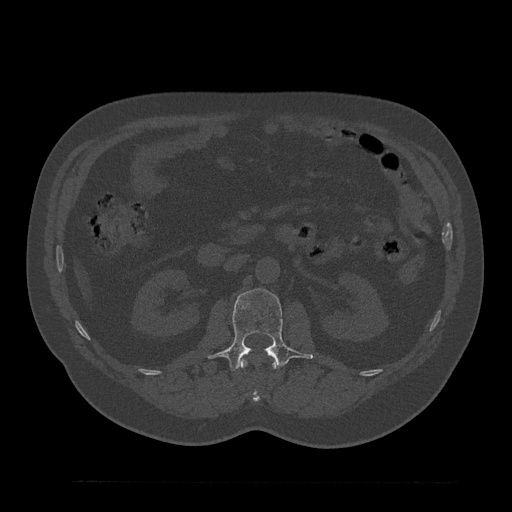
CT including the spine, one axial slice; position 113 of 797 along the scan axis; 120 kVp; bone window (W 1800 / L 400 HU); 512 × 512 image matrix, field of view 430 × 430 mm. Male patient, age 61 years. Case-level facts recorded for this patient, not image findings: primary cancer: prostate.
Annotated regions visible in this slice (semi-automatic segmentation, software-assisted and operator-edited):
- L1 vertebra: bounding box [x1, y1, x2, y2] px = [241, 354, 277, 402]
- L2 vertebra: [209, 288, 313, 372]